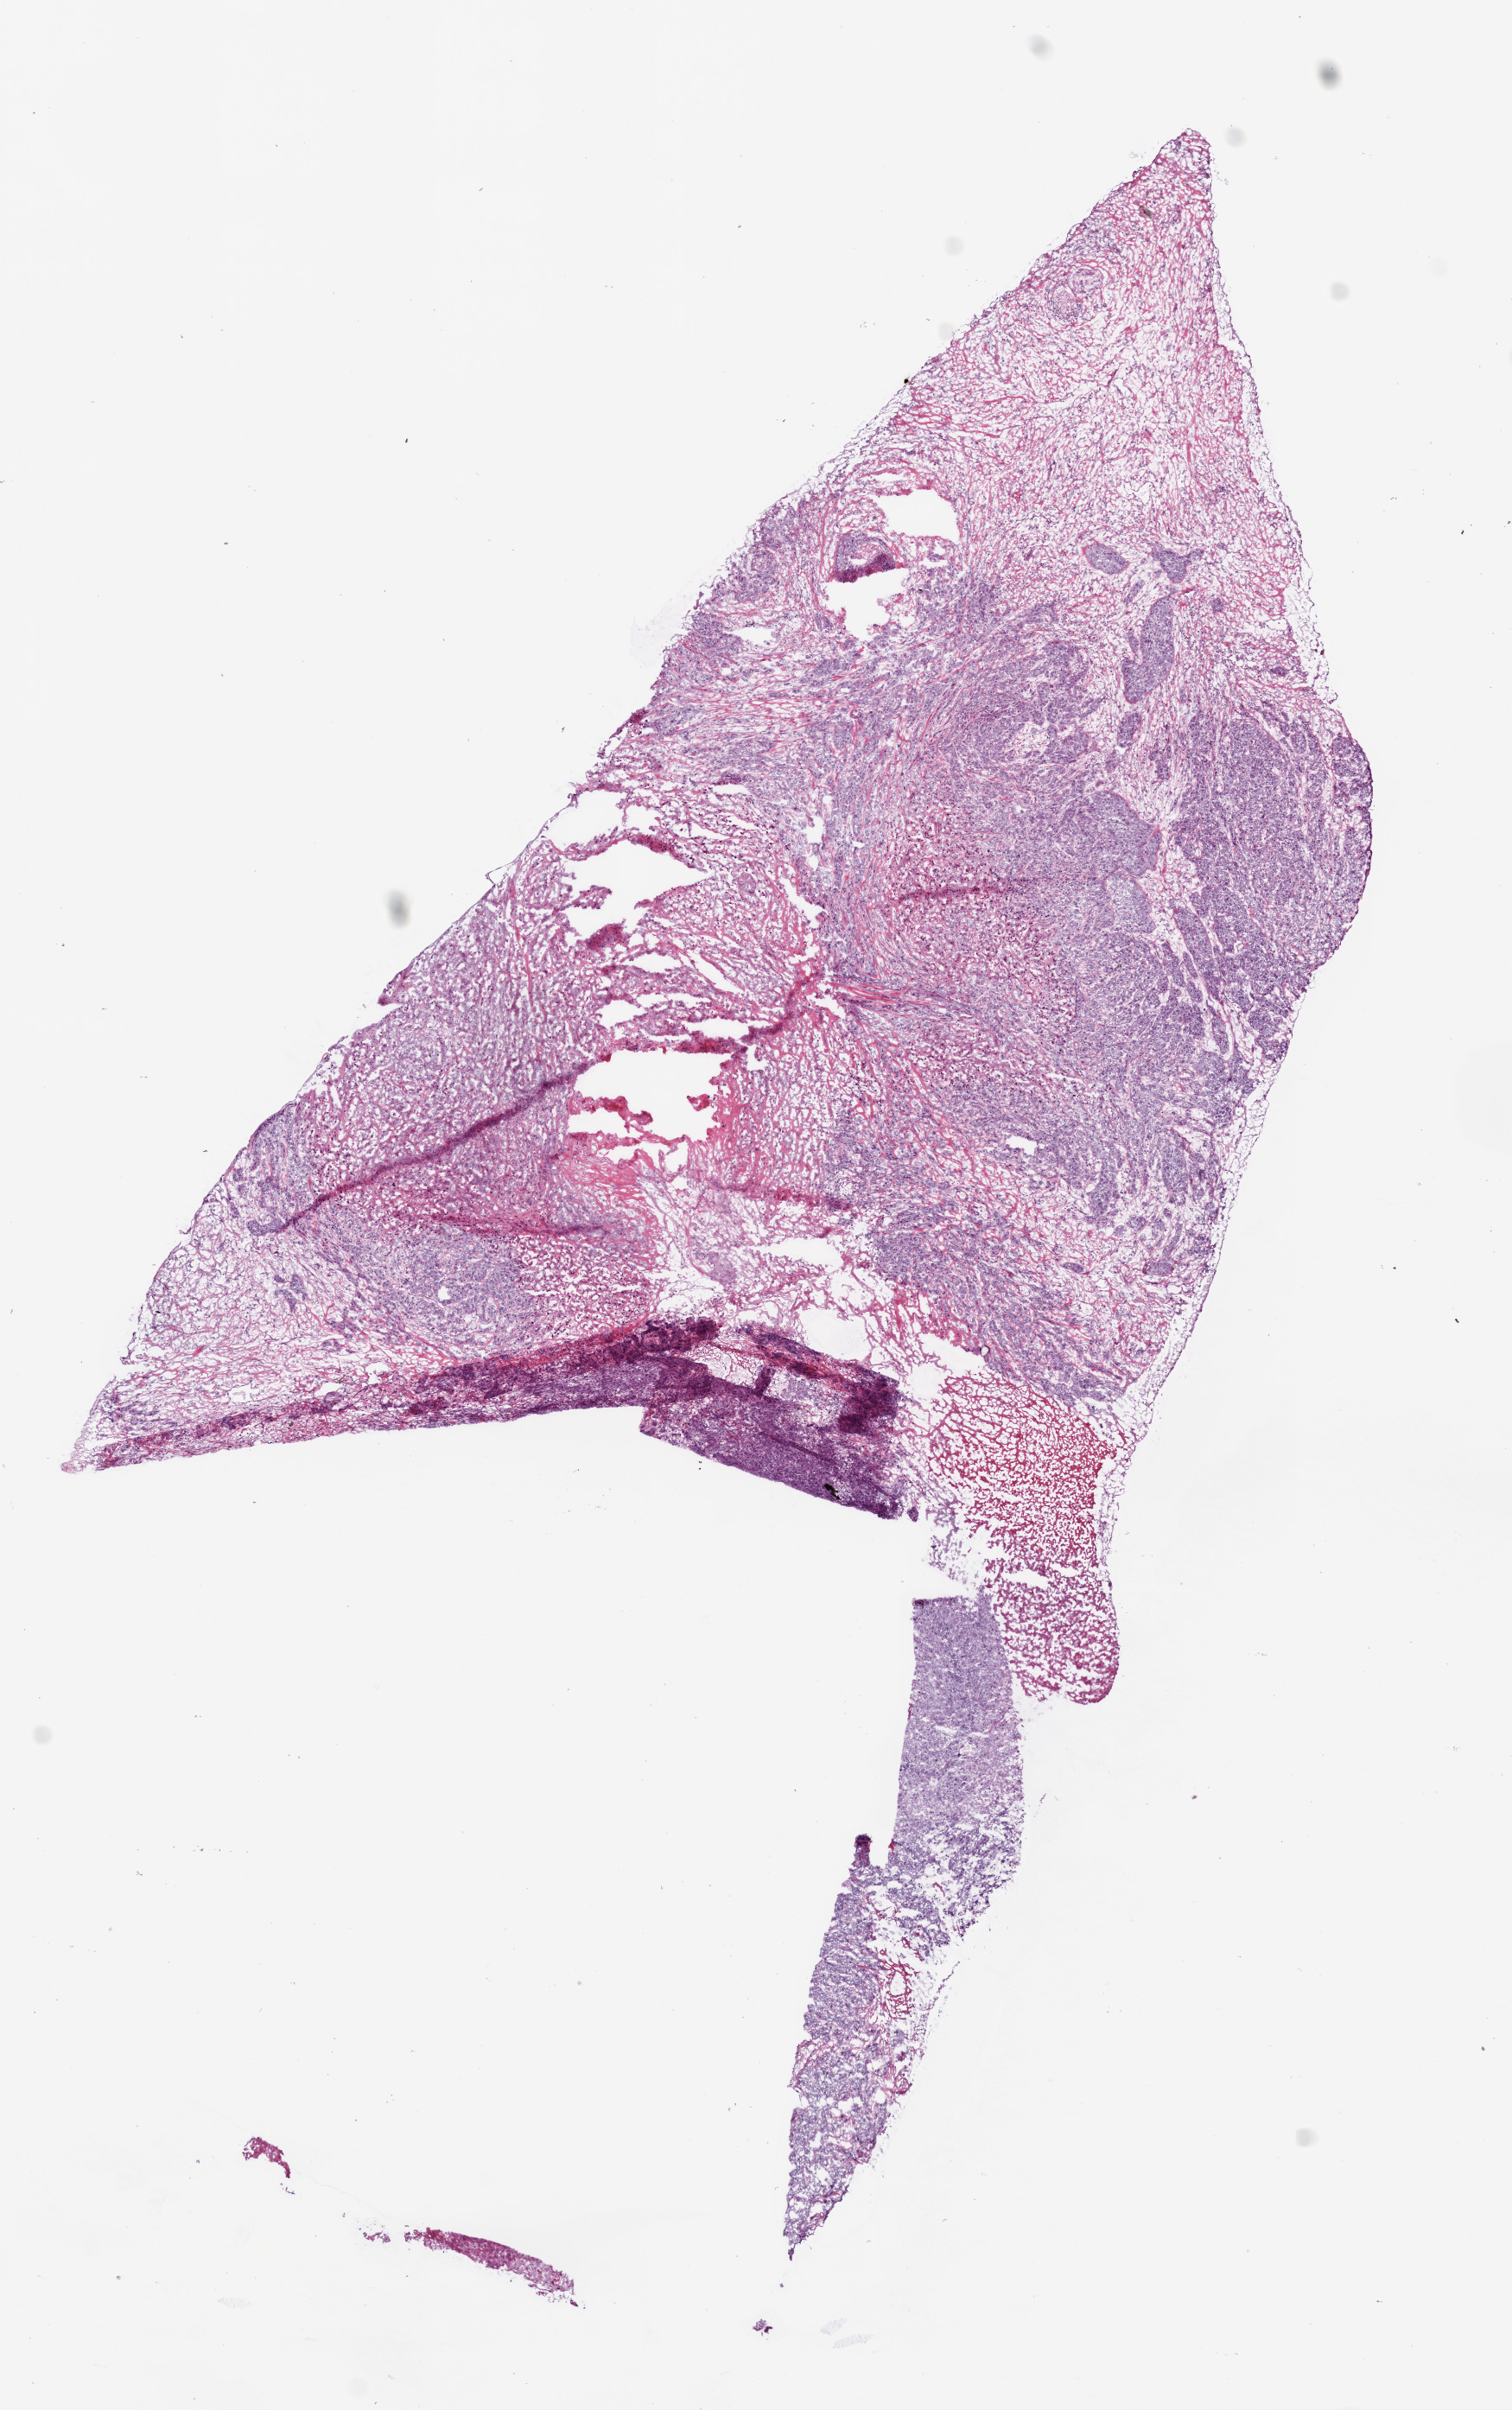
Digitized H&E tissue section (whole slide) — shown as a low-resolution overview of the whole scanned area (about 7.0 x 11.2 mm, from a 20x scan). Frozen section from the bottom of the tissue portion. Head and neck, primary tumour sample. Male patient; age at initial diagnosis 49 years. Histologic grade: G2 (moderately differentiated). Pathologist review of this section (percent, as recorded): tumour cells 70%, tumour nuclei 80%, normal cells 0%, stromal cells 15%, necrosis 15%.
• lymph nodes positive (case pathology): 0 of 48 examined
• AJCC pathologic stage: III (6th edition)
• histologic diagnosis: Squamous cell carcinoma, NOS (tongue, NOS)